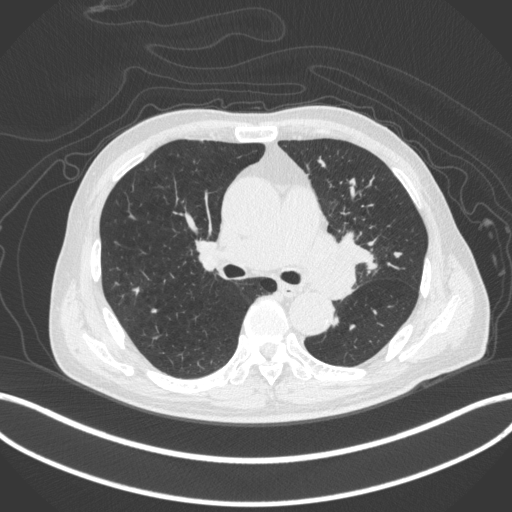
Chest CT, one axial slice; position 260 of 420 along the scan axis; 120 kVp; lung window (W 1500 / L -600 HU); 512 × 512 image matrix. Male patient, age 77 years. From the clinical record (not read from this slice): clinical TNM (as recorded): T3 N1 M0.
Outlined on this slice (bounding box drawn by a radiologist):
- lung tumour (recorded histology: adenocarcinoma): bounding box [x1, y1, x2, y2] px = [295, 222, 361, 303]